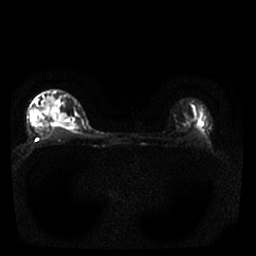
Breast MRI, one axial slice. Slice 22 of 25 in the series (ordered by position). Diffusion-weighted series; image 2 of 4 stored at this slice position (different b-values; order by instance number). 1.5 T. 256 × 256 image matrix. Female patient.
Outlined on this slice (manually delineated by an expert):
- tumour on diffusion-weighted imaging: bounding box (x1, y1, x2, y2) in pixels: (56, 113, 66, 125)